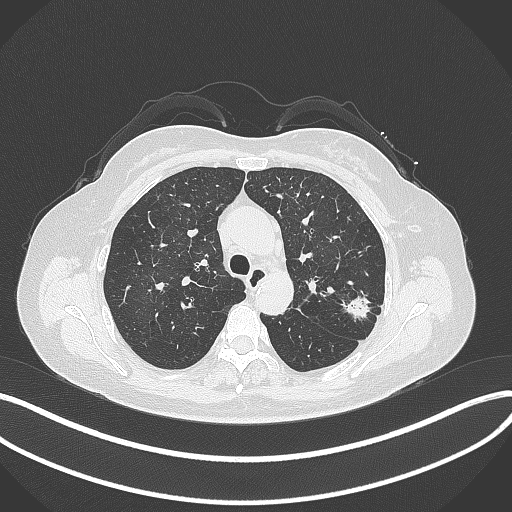
Chest CT, one axial slice; slice 230 of 319 in the series (ordered by position); 120 kVp; lung window (W 1500 / L -600 HU); 1 mm slice thickness; 512 × 512 image matrix, field of view 400 × 400 mm. Patient: female, 60 years. Case-level facts recorded for this patient, not image findings: clinical TNM (as recorded): T1c N0 M0.
Structures marked on this image (rectangle marked by the reading radiologist):
- lung tumour (recorded histology: adenocarcinoma): bounding box <340,291,372,325> (left, top, right, bottom; pixels)